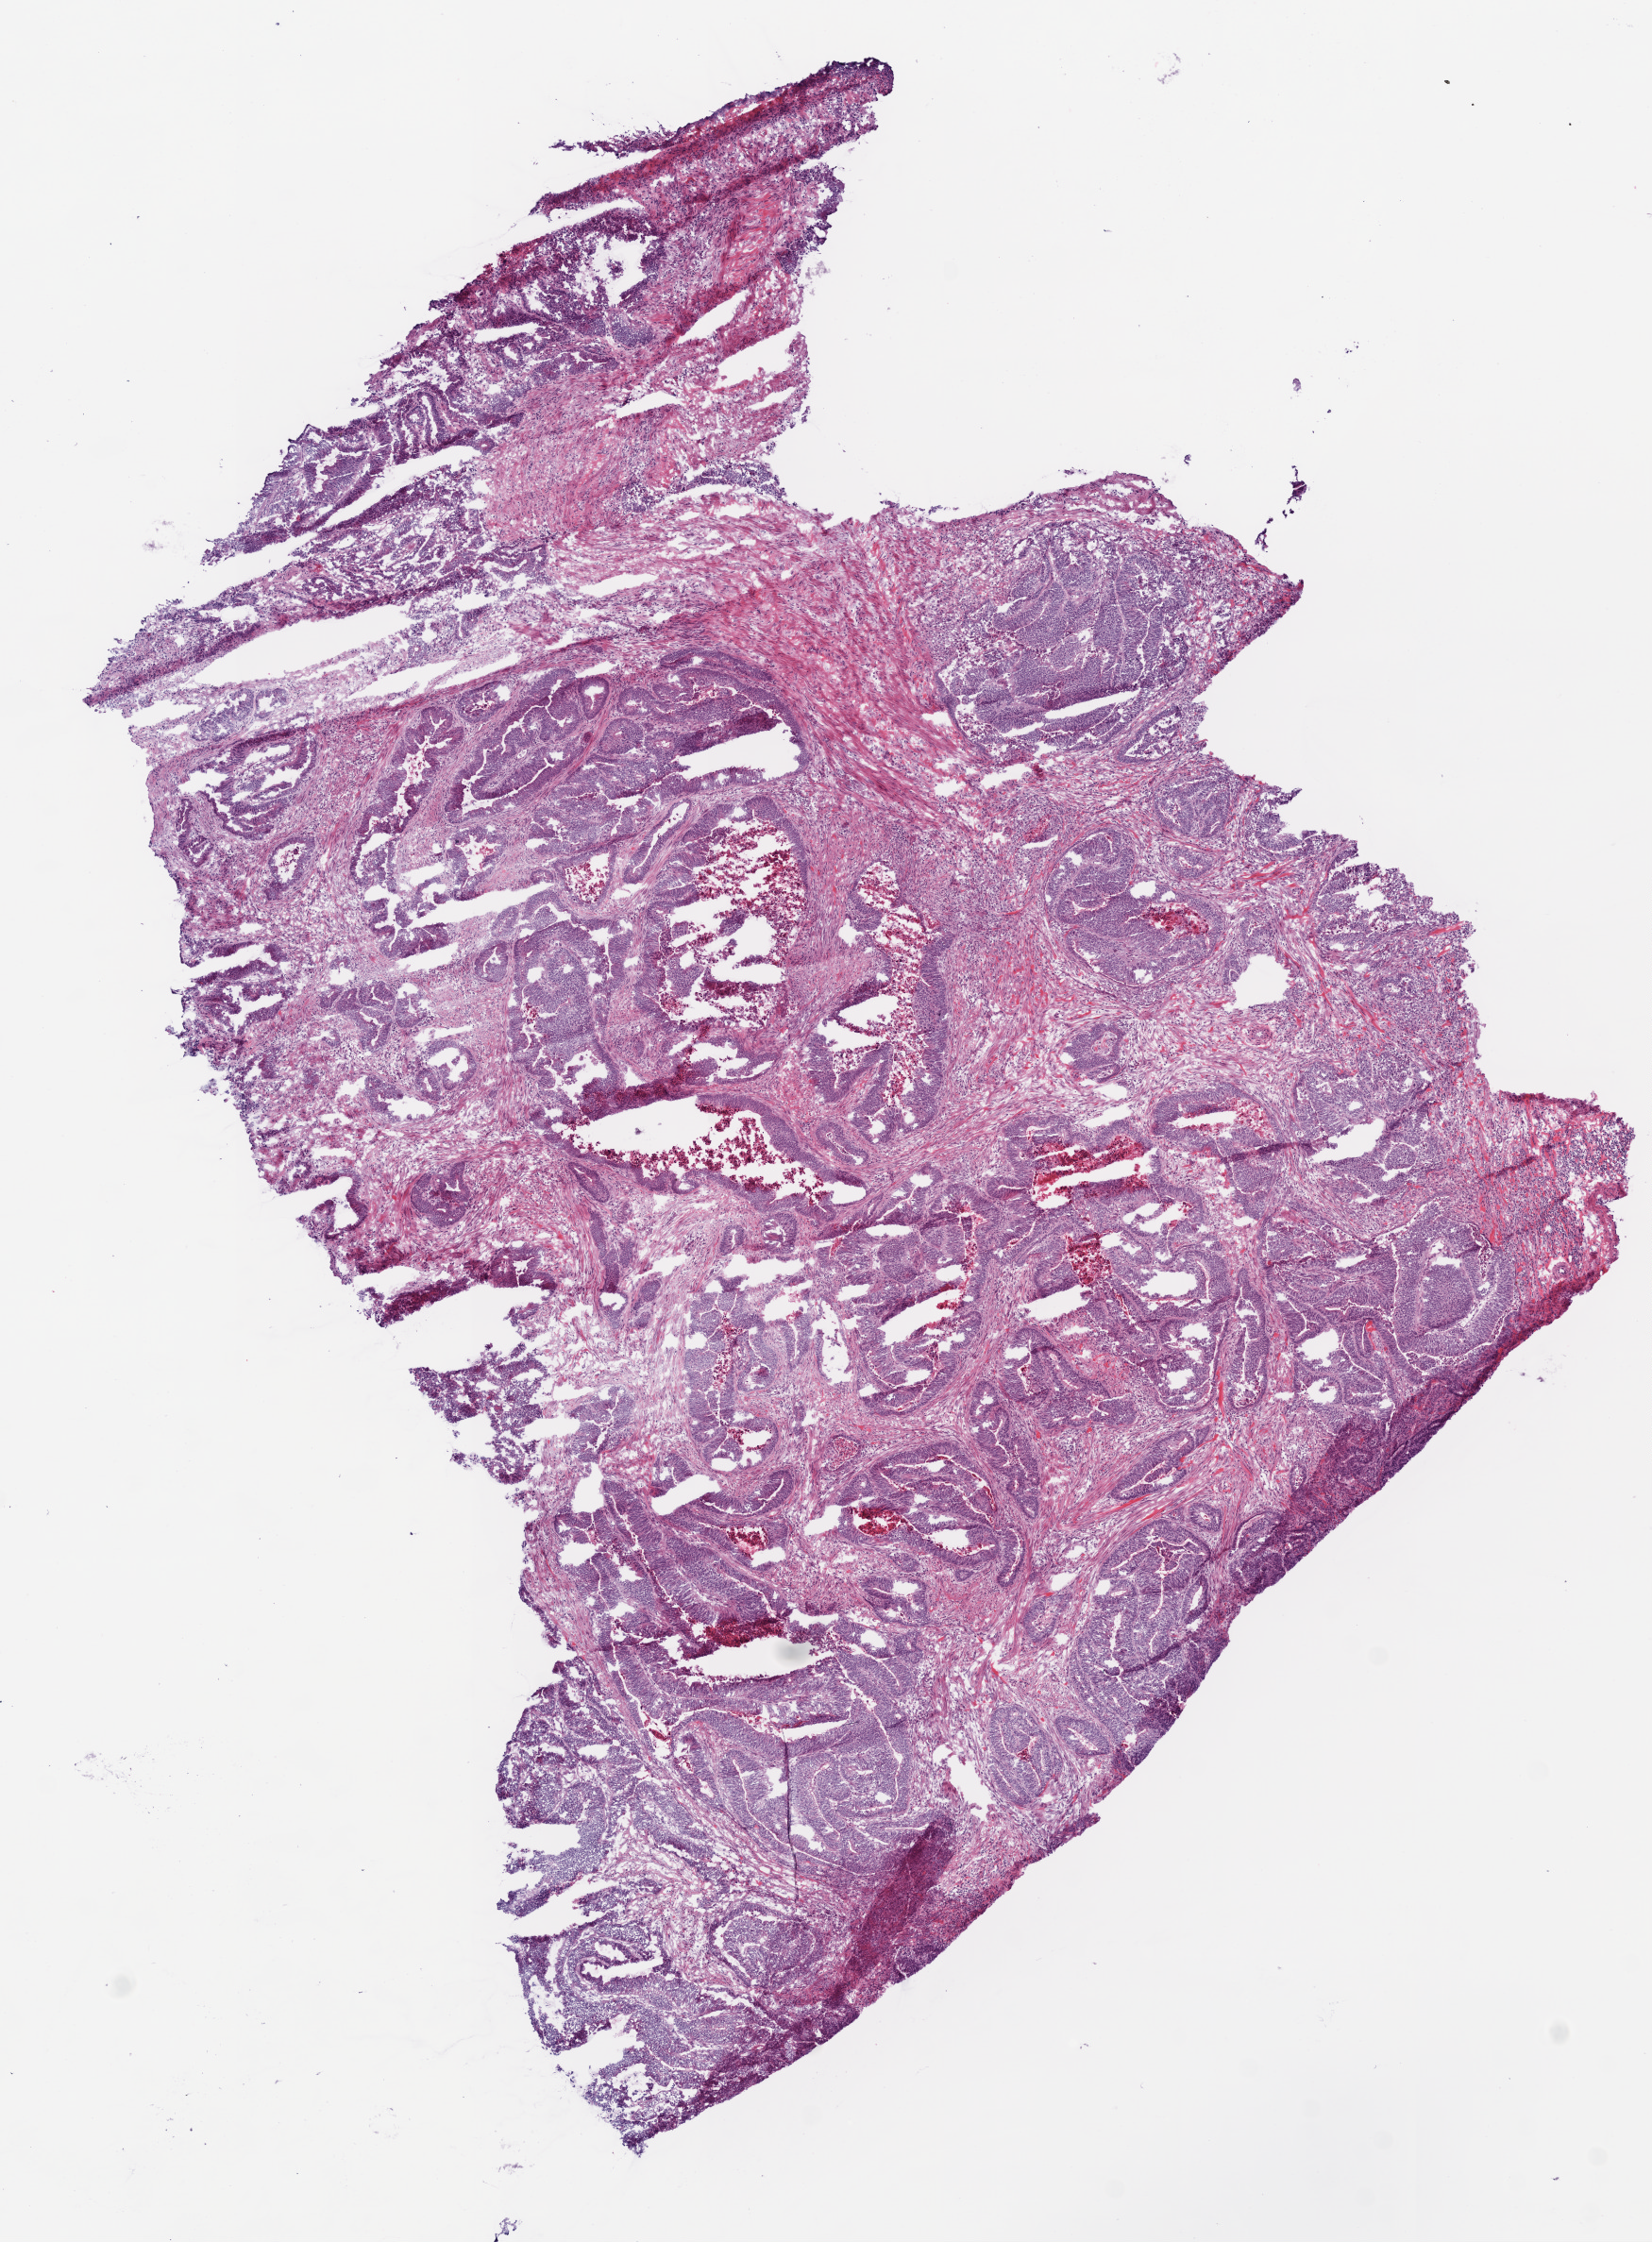
H&E whole-slide image, low-resolution overview of the scanned area, about 7.0 x 9.5 mm. Frozen section from the bottom of the tissue portion. Sample: primary tumour, colon. Female patient; age at initial diagnosis 41 years.
Diagnosis: Adenocarcinoma, NOS.